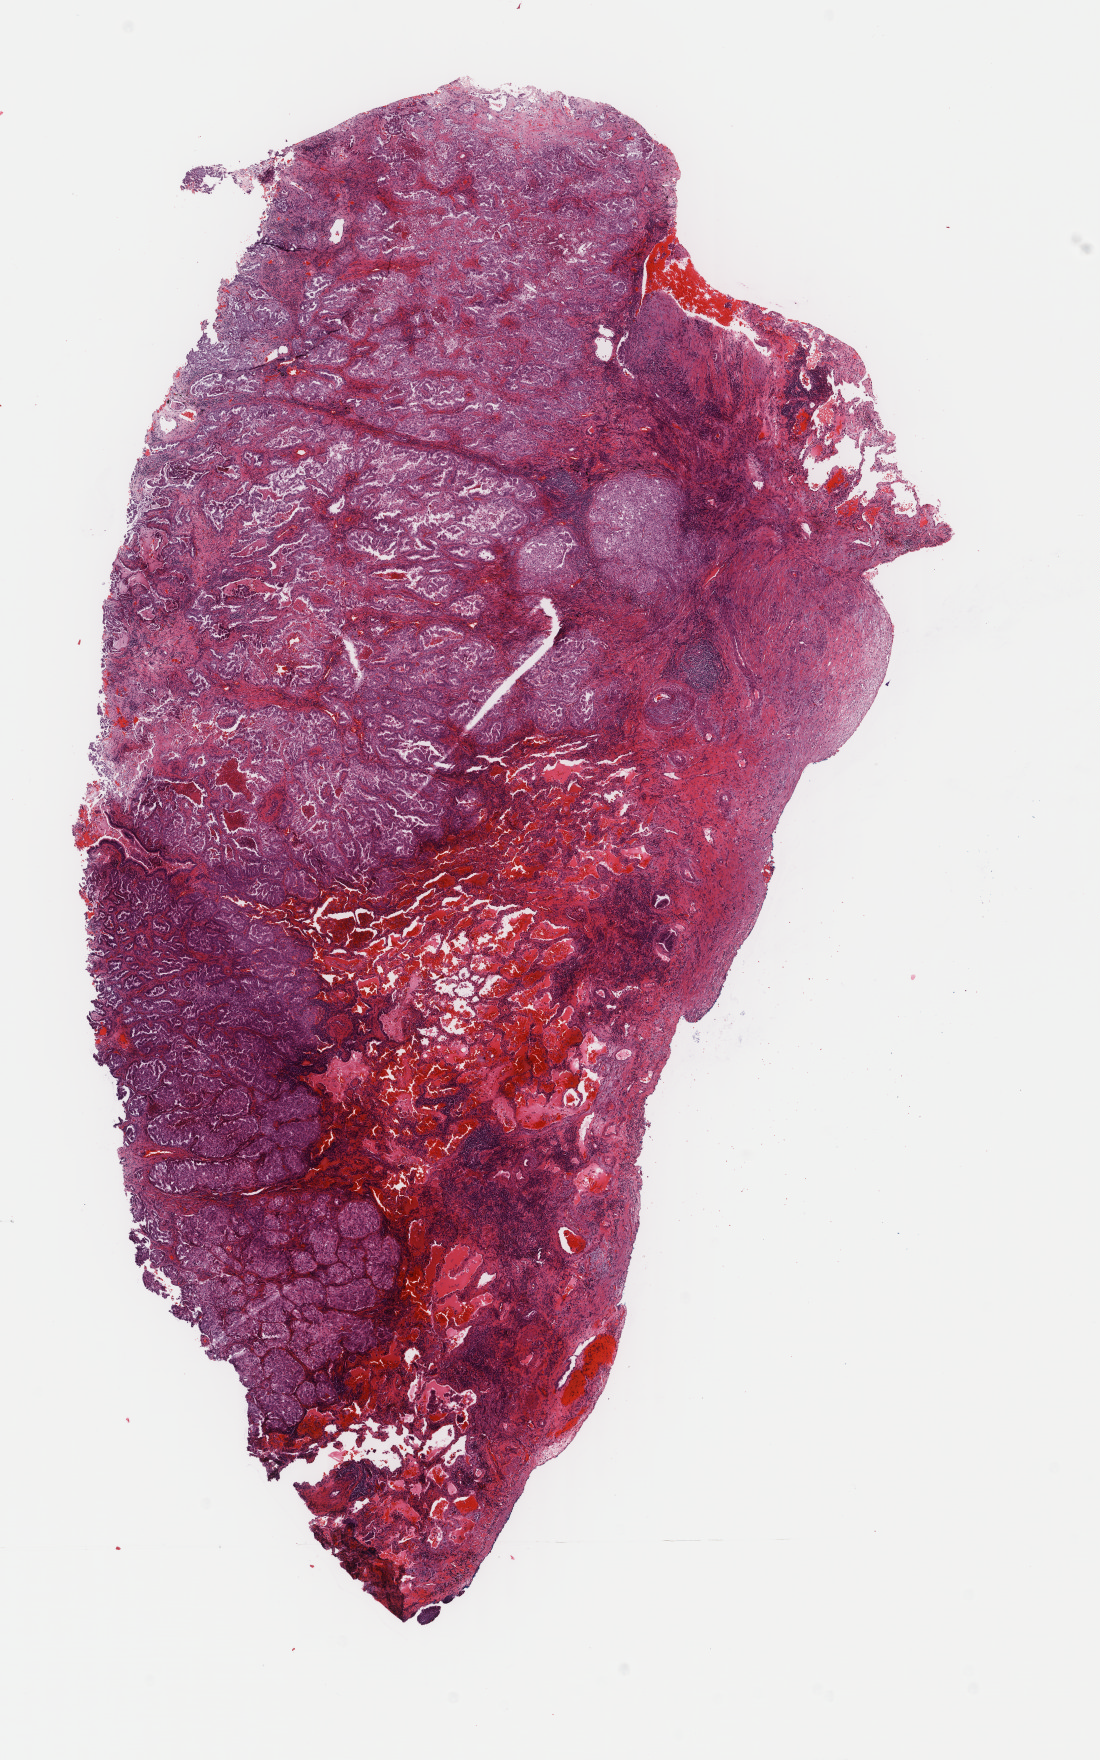
Digitized H&E tissue section (whole slide), whole scanned area (about 8.7 x 14.0 mm, from a 40x scan) shown as a low-resolution overview; frozen section; sample: primary tumour, lung. Female, age 60 years at initial diagnosis. Slide review estimates, as recorded: tumour cells 65%, tumour nuclei 65%, normal cells 2%, stromal cells 31%, necrosis 2%. Infiltration values recorded for this section: lymphocyte infiltration 5%, monocyte infiltration 3%, neutrophil infiltration 2%.
Laterality: right. Pathologic diagnosis: Adenocarcinoma, NOS (upper lobe, lung). AJCC pathologic stage: IB (6th edition).